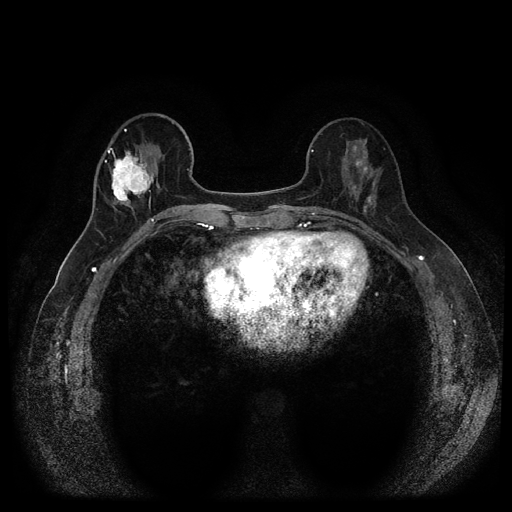
Breast MRI (dynamic contrast-enhanced, multi-phase), one axial slice. Slice 39 of 116 in the series (ordered by position). Dynamic contrast-enhanced series, time point 2 of 5 at this slice position (early post-contrast). 1.5 T. TE 2.6 ms, TR 5.4 ms. 512 × 512 image matrix, field of view 340 × 340 mm. Female patient, age 56 years.
Outlined on this slice (semi-automatic segmentation, software-assisted and operator-edited):
- breast lesion (labelled benign in the annotation): bounding box (x1, y1, x2, y2) in pixels: (355, 152, 368, 174)
- breast lesion (labelled 'tumour' in the annotation; benign lesions carry a separate 'benign' label): (108, 145, 159, 210)